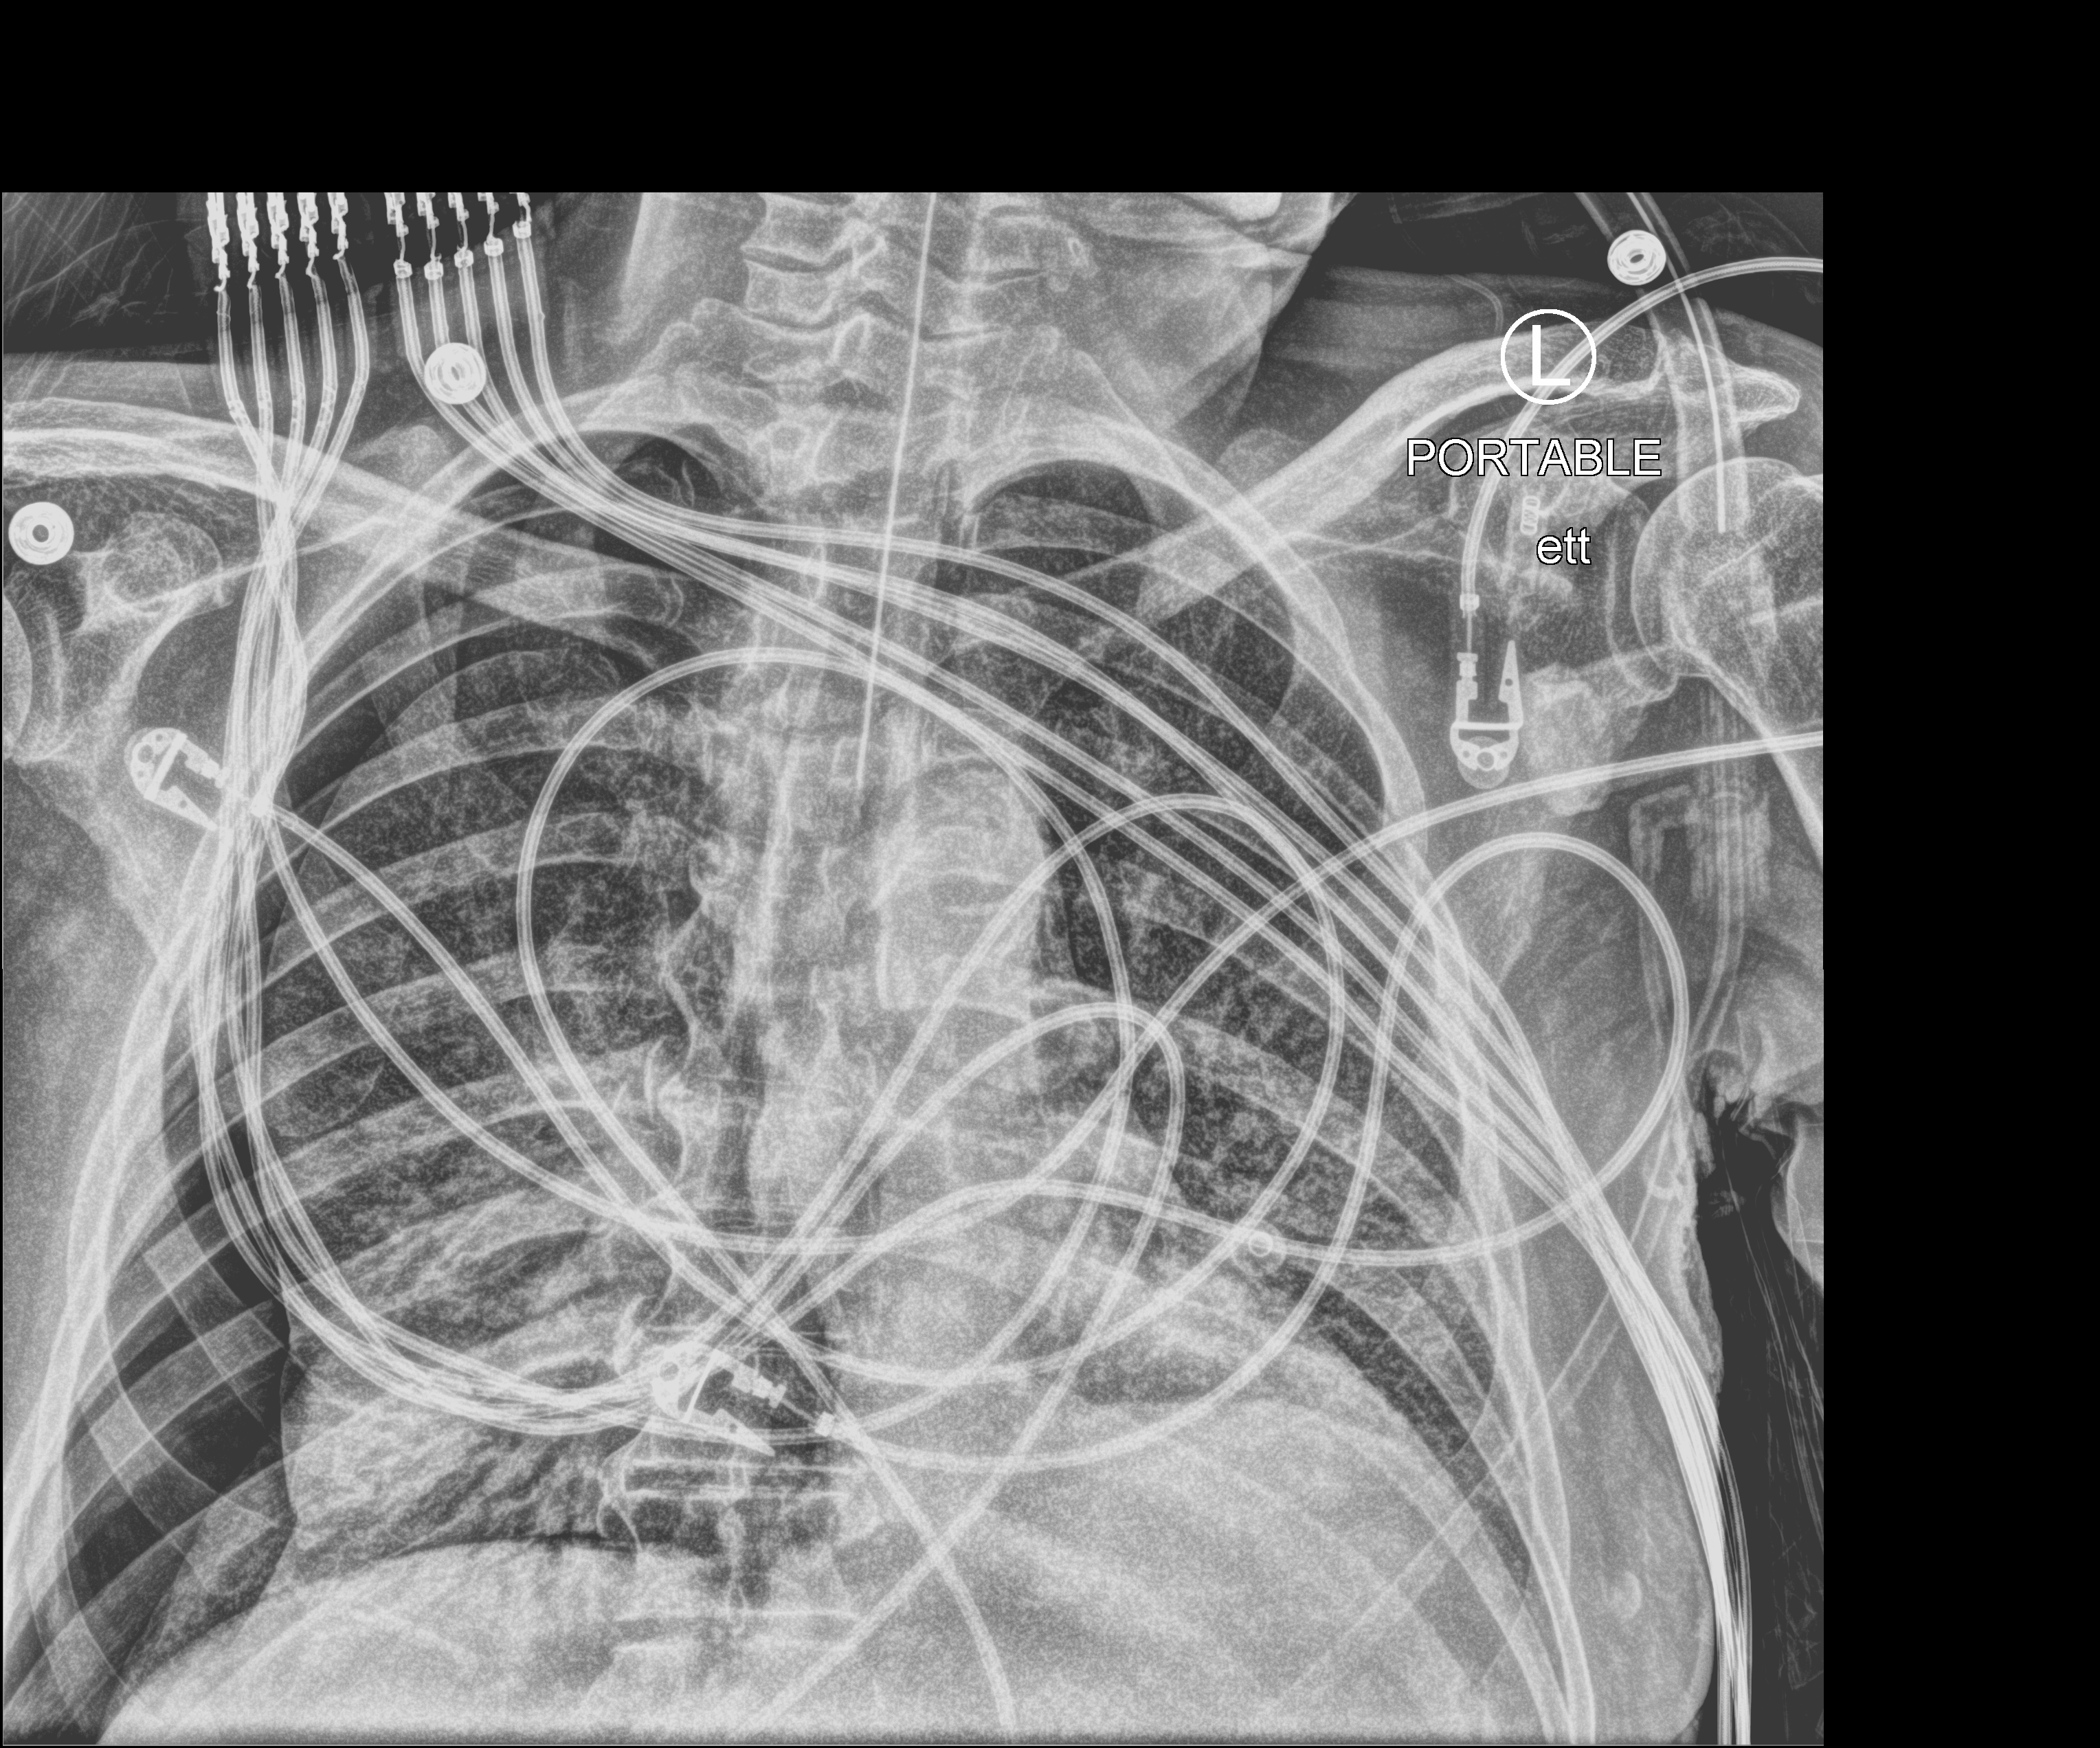
Portable chest radiograph; anteroposterior (AP) projection. Patient hospitalised with COVID-19; male, aged 75–90 years.
Hospital-stay facts (about this admission, not read from this image; timing relative to this image not recorded):
- admitted to intensive care during this hospital stay: yes